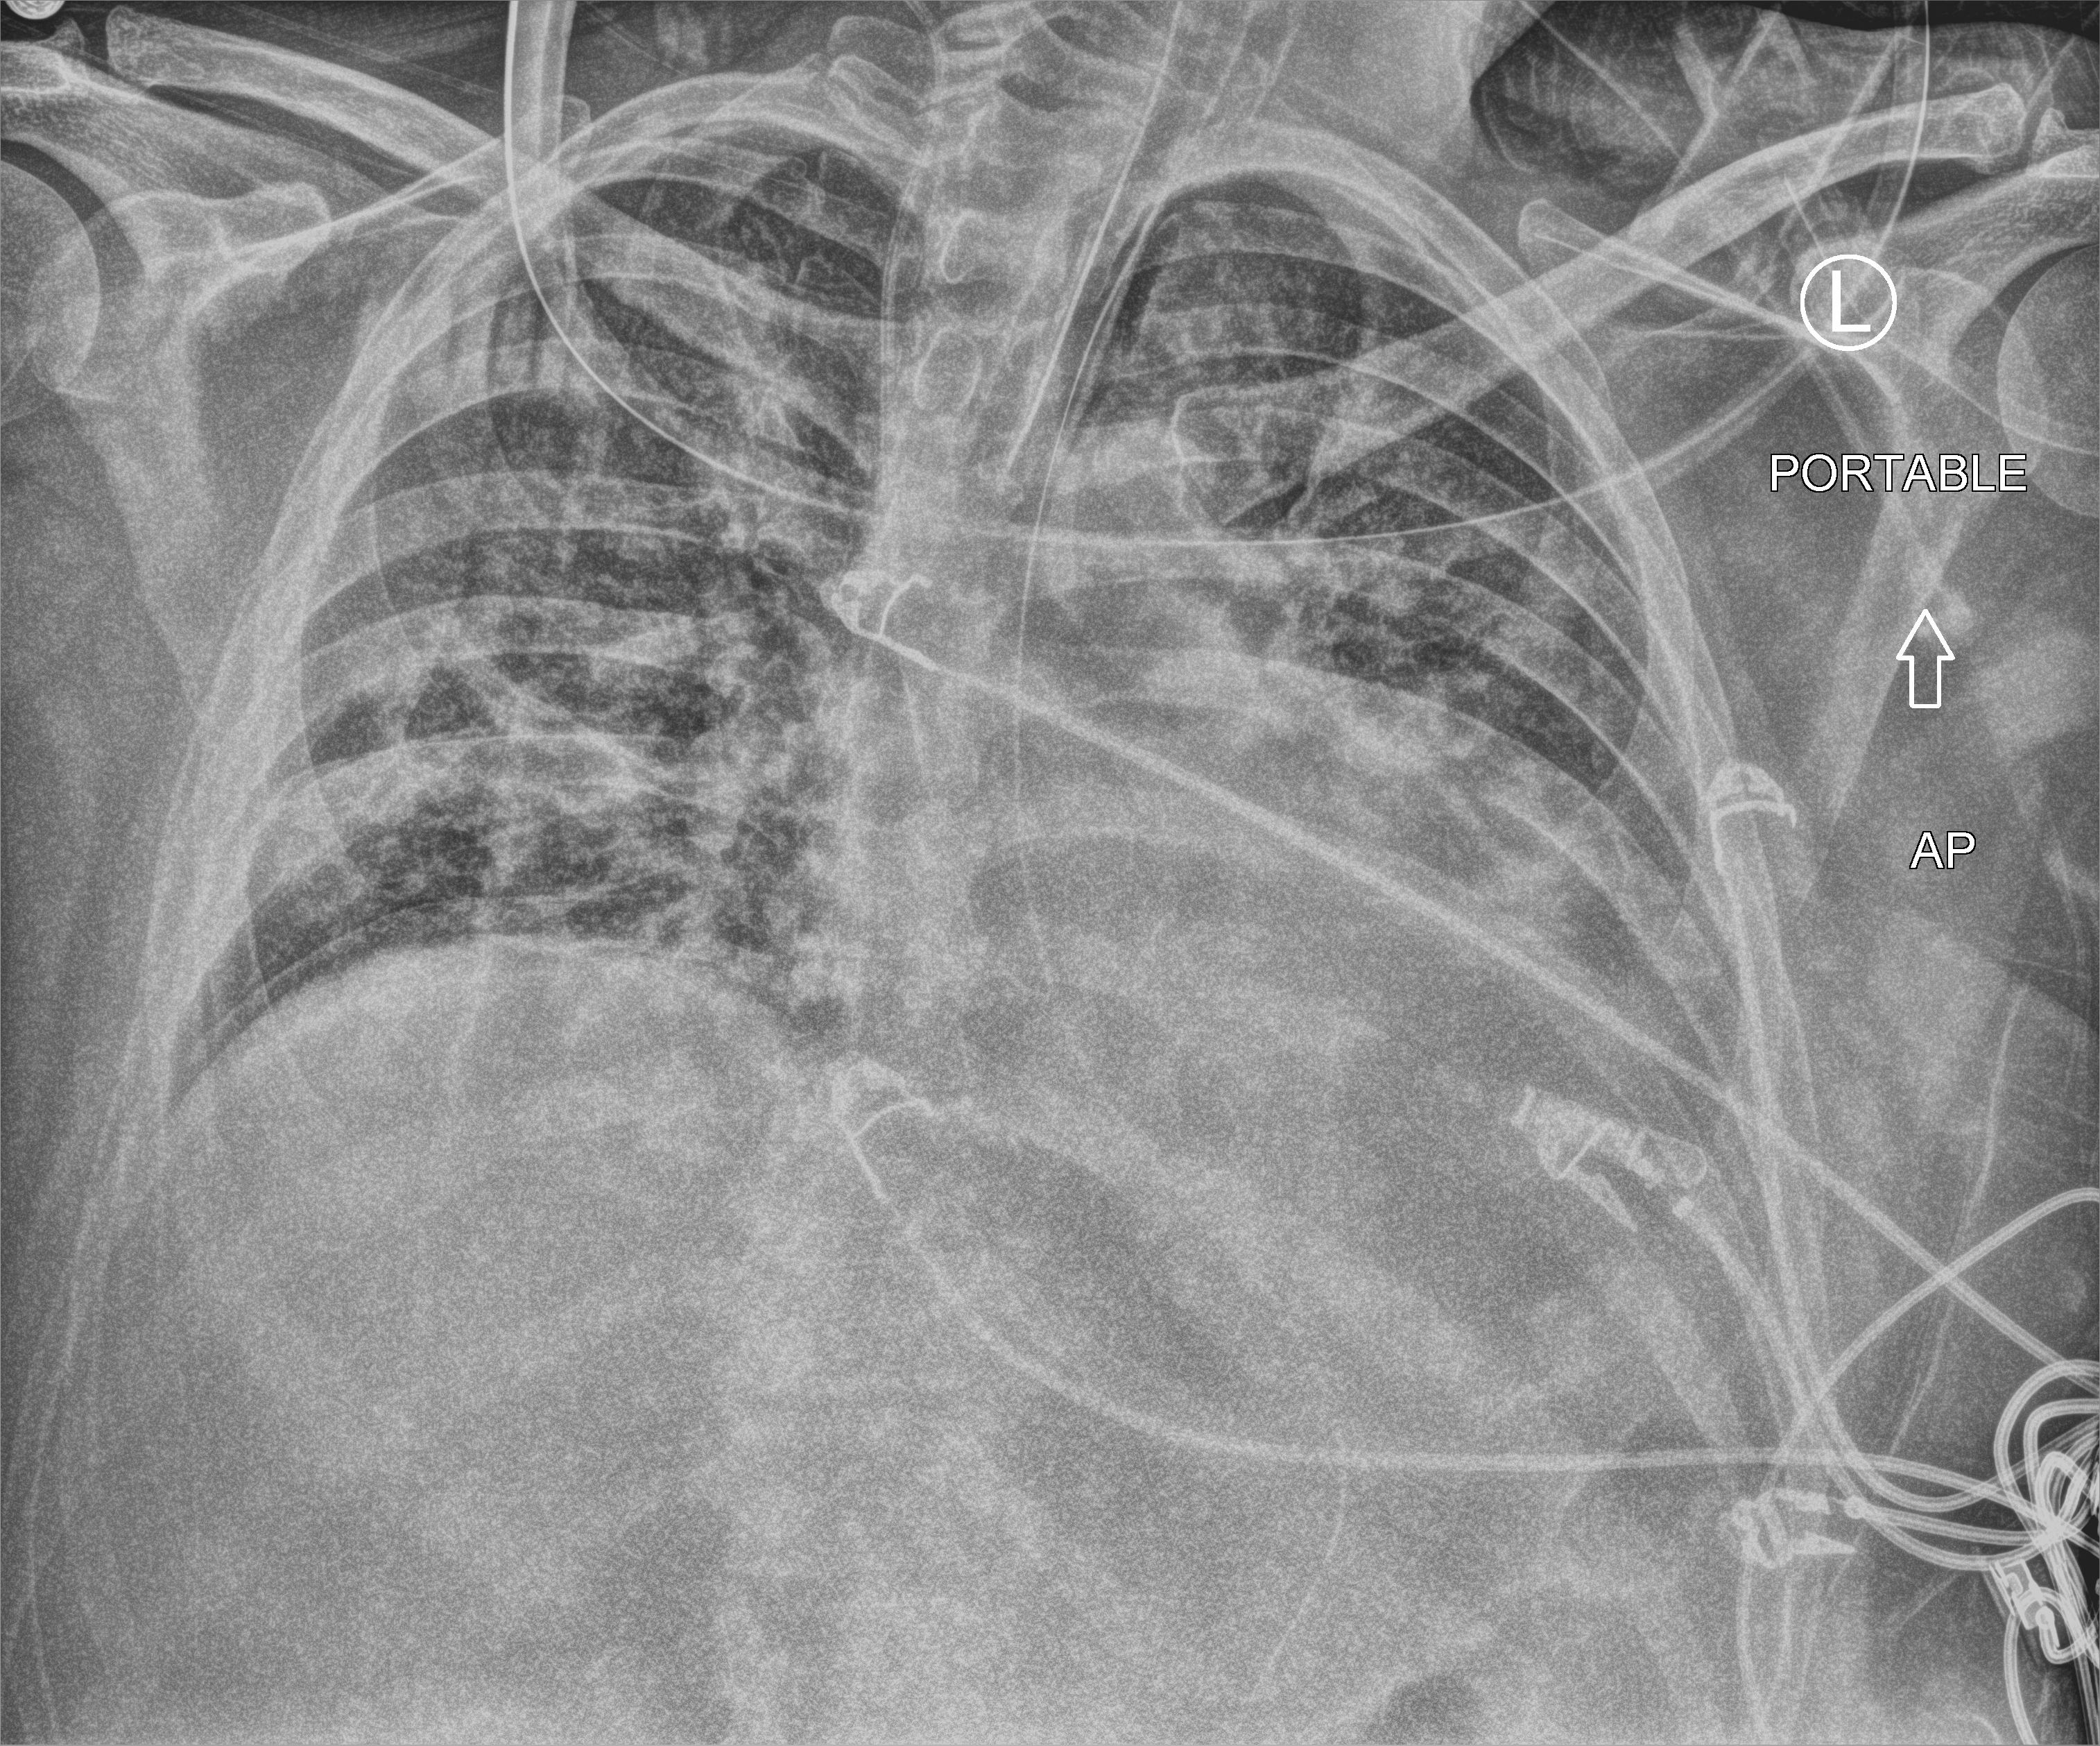
Portable chest radiograph, anteroposterior (AP) projection. Patient hospitalised with COVID-19; male, aged 18–59 years.
From the hospital-stay record, not from the radiograph (when in the stay this image was taken is not recorded): admitted to intensive care during this hospital stay: yes; COPD (admission record): no.